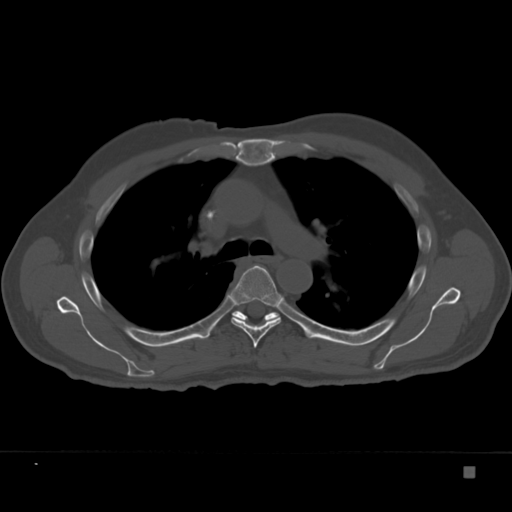
CT including the spine, one axial slice; position 252 of 332 along the scan axis; bone window (W 1800 / L 400 HU); 512 × 512 image matrix, field of view 389 × 389 mm. Patient: male, 72 years. From the clinical record (not read from this slice): primary cancer: skeletal.
Annotated regions visible in this slice (semi-automatic segmentation, software-assisted and operator-edited):
- T5 vertebra: bounding box [x1, y1, x2, y2] px = [228, 265, 283, 348]
- T6 vertebra: [213, 311, 281, 329]